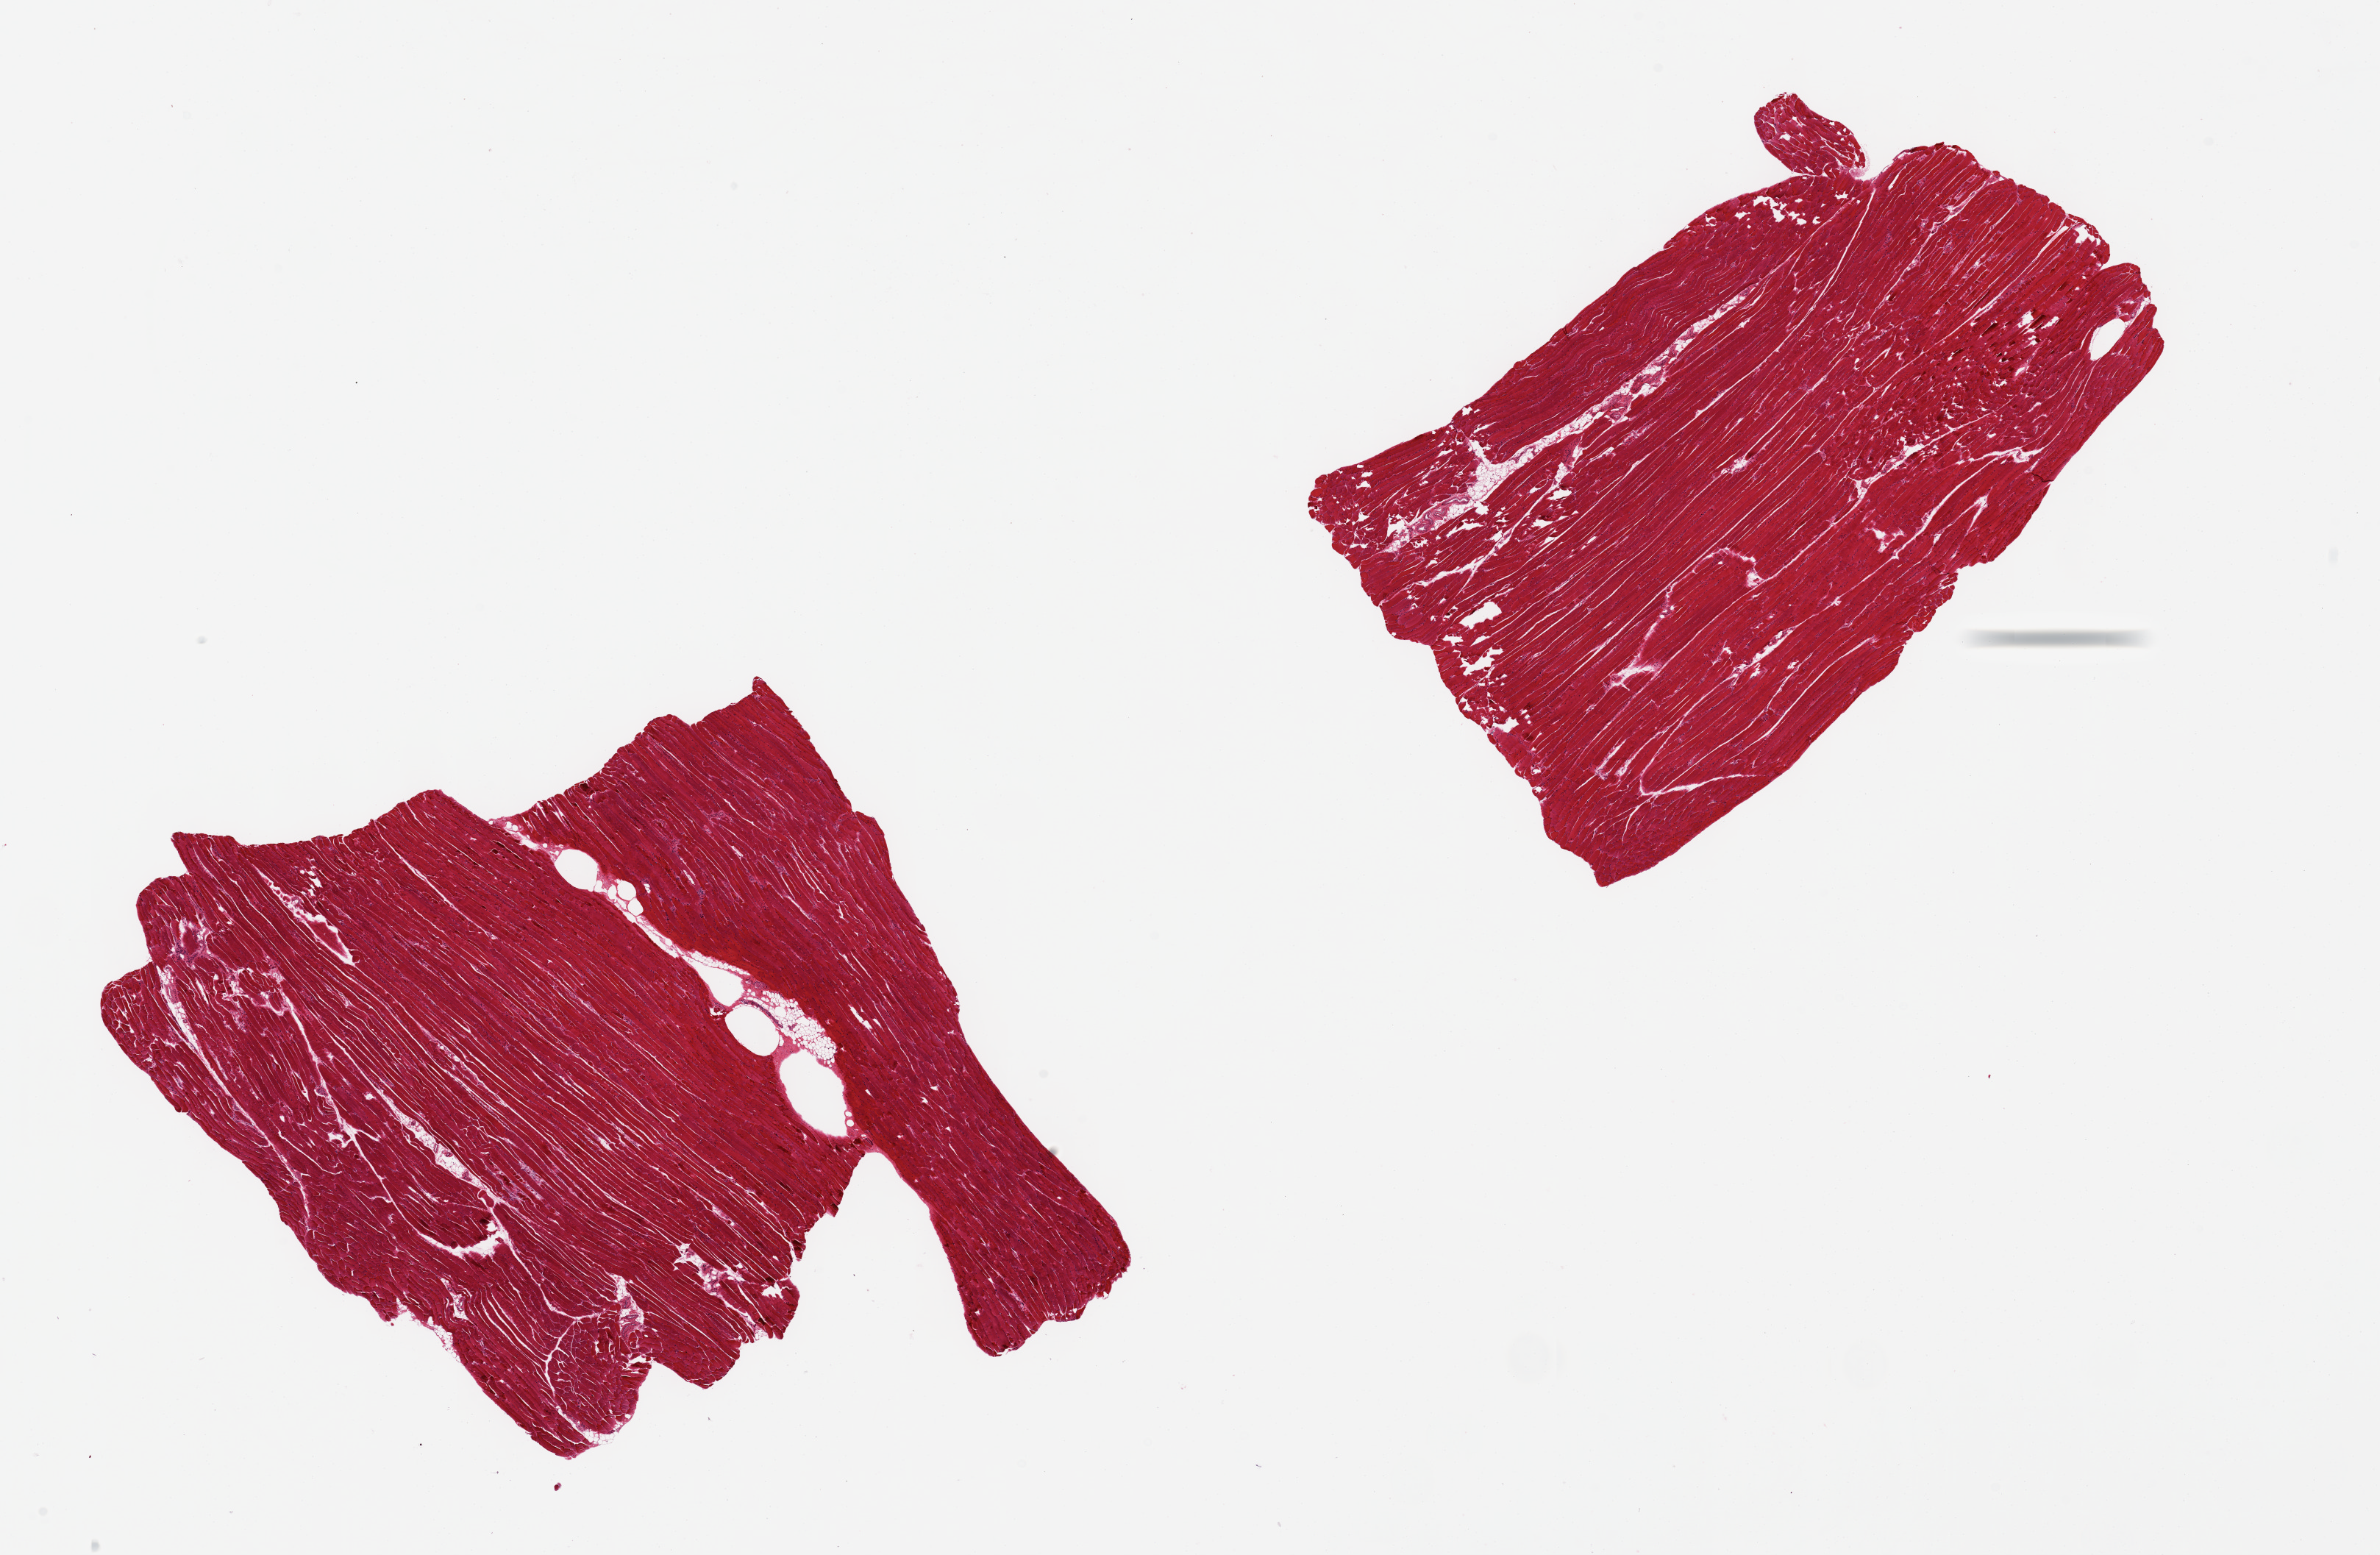
Haematoxylin and eosin whole-slide image, brightfield, low-resolution overview of the scanned area, about 25.6 x 16.7 mm, PAXgene-fixed, paraffin-embedded tissue, target tissue: skeletal muscle, donor tissue sample. Donor sex: female.
Review note (as recorded): 2 ~8x7mm pieces, small areas of poor fixation with tears.